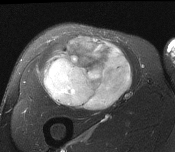
MRI of an extremity soft-tissue mass, one axial slice. Slice 95 of 116 in the series (ordered by position). T2-weighted fat-saturated. MR volume resampled by the dataset authors to the PET/CT grid (not the native acquisition matrix). 175 × 152 image matrix. Male patient. From the clinical record (not read from this slice): histological type: pleiomorphic leiomyosarcoma; grade: intermediate; site of the primary tumour: right thigh.
Annotated regions visible in this slice (expert contour drawn on MRI and transferred to this co-registered scan by the dataset authors):
- gross tumour volume including surrounding oedema: box from (x=42, y=36) to (x=134, y=112) px
- gross tumour volume (mass): (x=44, y=36)–(x=134, y=112)